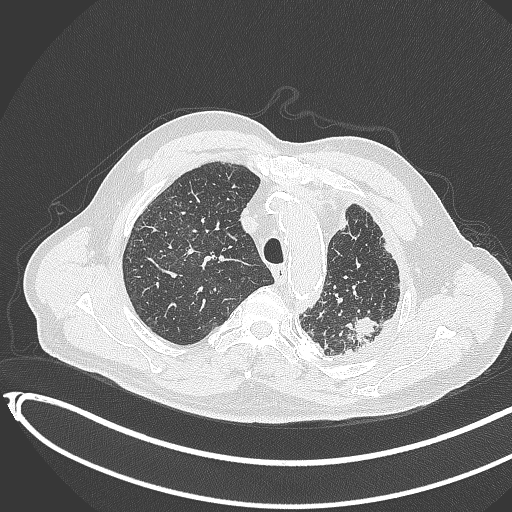
Chest CT, one axial slice; reconstruction kernel B70f; 120 kVp; lung window (W 1500 / L -600 HU); 1 mm slice thickness; 512 × 512 image matrix. Male patient, age 78 years. From the clinical record (not read from this slice): clinical TNM (as recorded): T1c N0 M1.
Structures marked on this image (rectangle marked by the reading radiologist):
- lung tumour (recorded histology: adenocarcinoma): bounding box (x1, y1, x2, y2) in pixels: (345, 316, 381, 346)